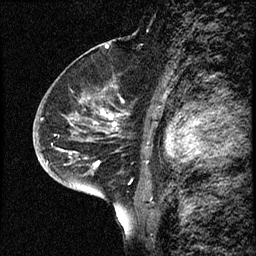
Breast MRI (dynamic contrast-enhanced), one sagittal slice. Slice 44 of 68 in the series (ordered by position). Dynamic contrast-enhanced study with each time point stored as its own series, time point 2 of 3 at this slice position (early post-contrast, ordered by acquisition time). 1.5 T. TE 4.2 ms, TR 17.6 ms. 256 × 256 image matrix, field of view 200 × 200 mm. Patient: female, 52 years. From the clinical record (not read from this slice): setting: breast cancer imaged before/during neoadjuvant chemotherapy; receptor status: HER2-positive.
Outlined on this slice (semi-automatic segmentation, software-assisted and operator-edited):
- analysis volume of interest (the breast-tissue region the enhancement analysis was run in; not a lesion): box from (x=50, y=61) to (x=130, y=184) px
- tumour enhancement mask (voxels above the 100 % enhancement threshold inside the analysis volume of interest): (x=96, y=110)–(x=113, y=166)